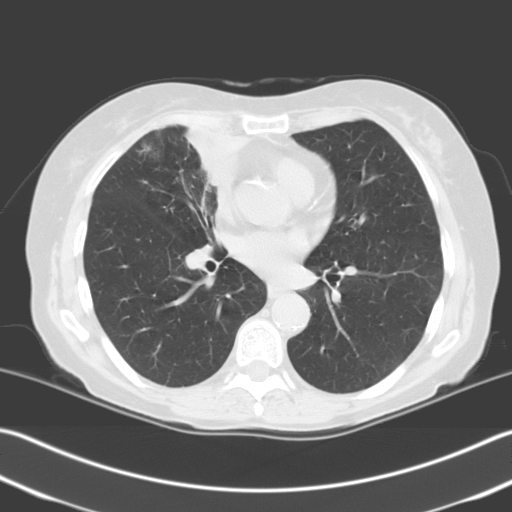
Low-dose screening chest CT, one axial slice; position 111 of 204 along the scan axis; 140 kVp; lung window (W 1500 / L -600 HU); 512 × 512 image matrix, field of view 348 × 348 mm.
Outlined on this slice (expert manual segmentation):
- lesion 1 (tumor, upper lobe of right lung): bounding box <186,131,246,185> (left, top, right, bottom; pixels)